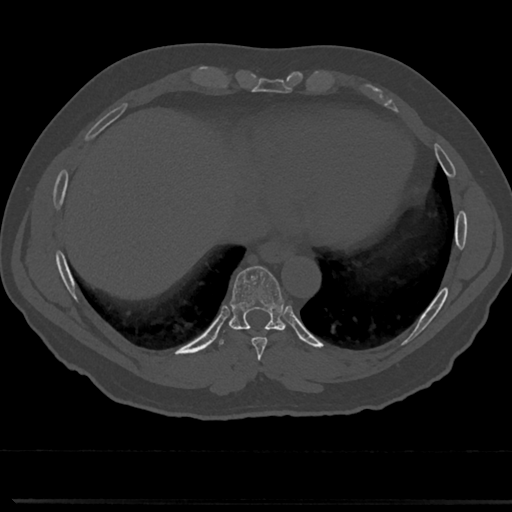
CT including the spine, one axial slice; slice 323 of 817 in the series (ordered by position); 120 kVp; bone window (W 1800 / L 400 HU); 0.5 mm slice thickness; 512 × 512 image matrix, field of view 355 × 355 mm. Male patient, age 61 years. Case-level facts recorded for this patient, not image findings: primary cancer: prostate.
Annotated regions visible in this slice (semi-automatic segmentation, software-assisted and operator-edited):
- T7 vertebra: box from (x=258, y=359) to (x=266, y=376) px
- T8 vertebra: (x=214, y=269)–(x=308, y=357)